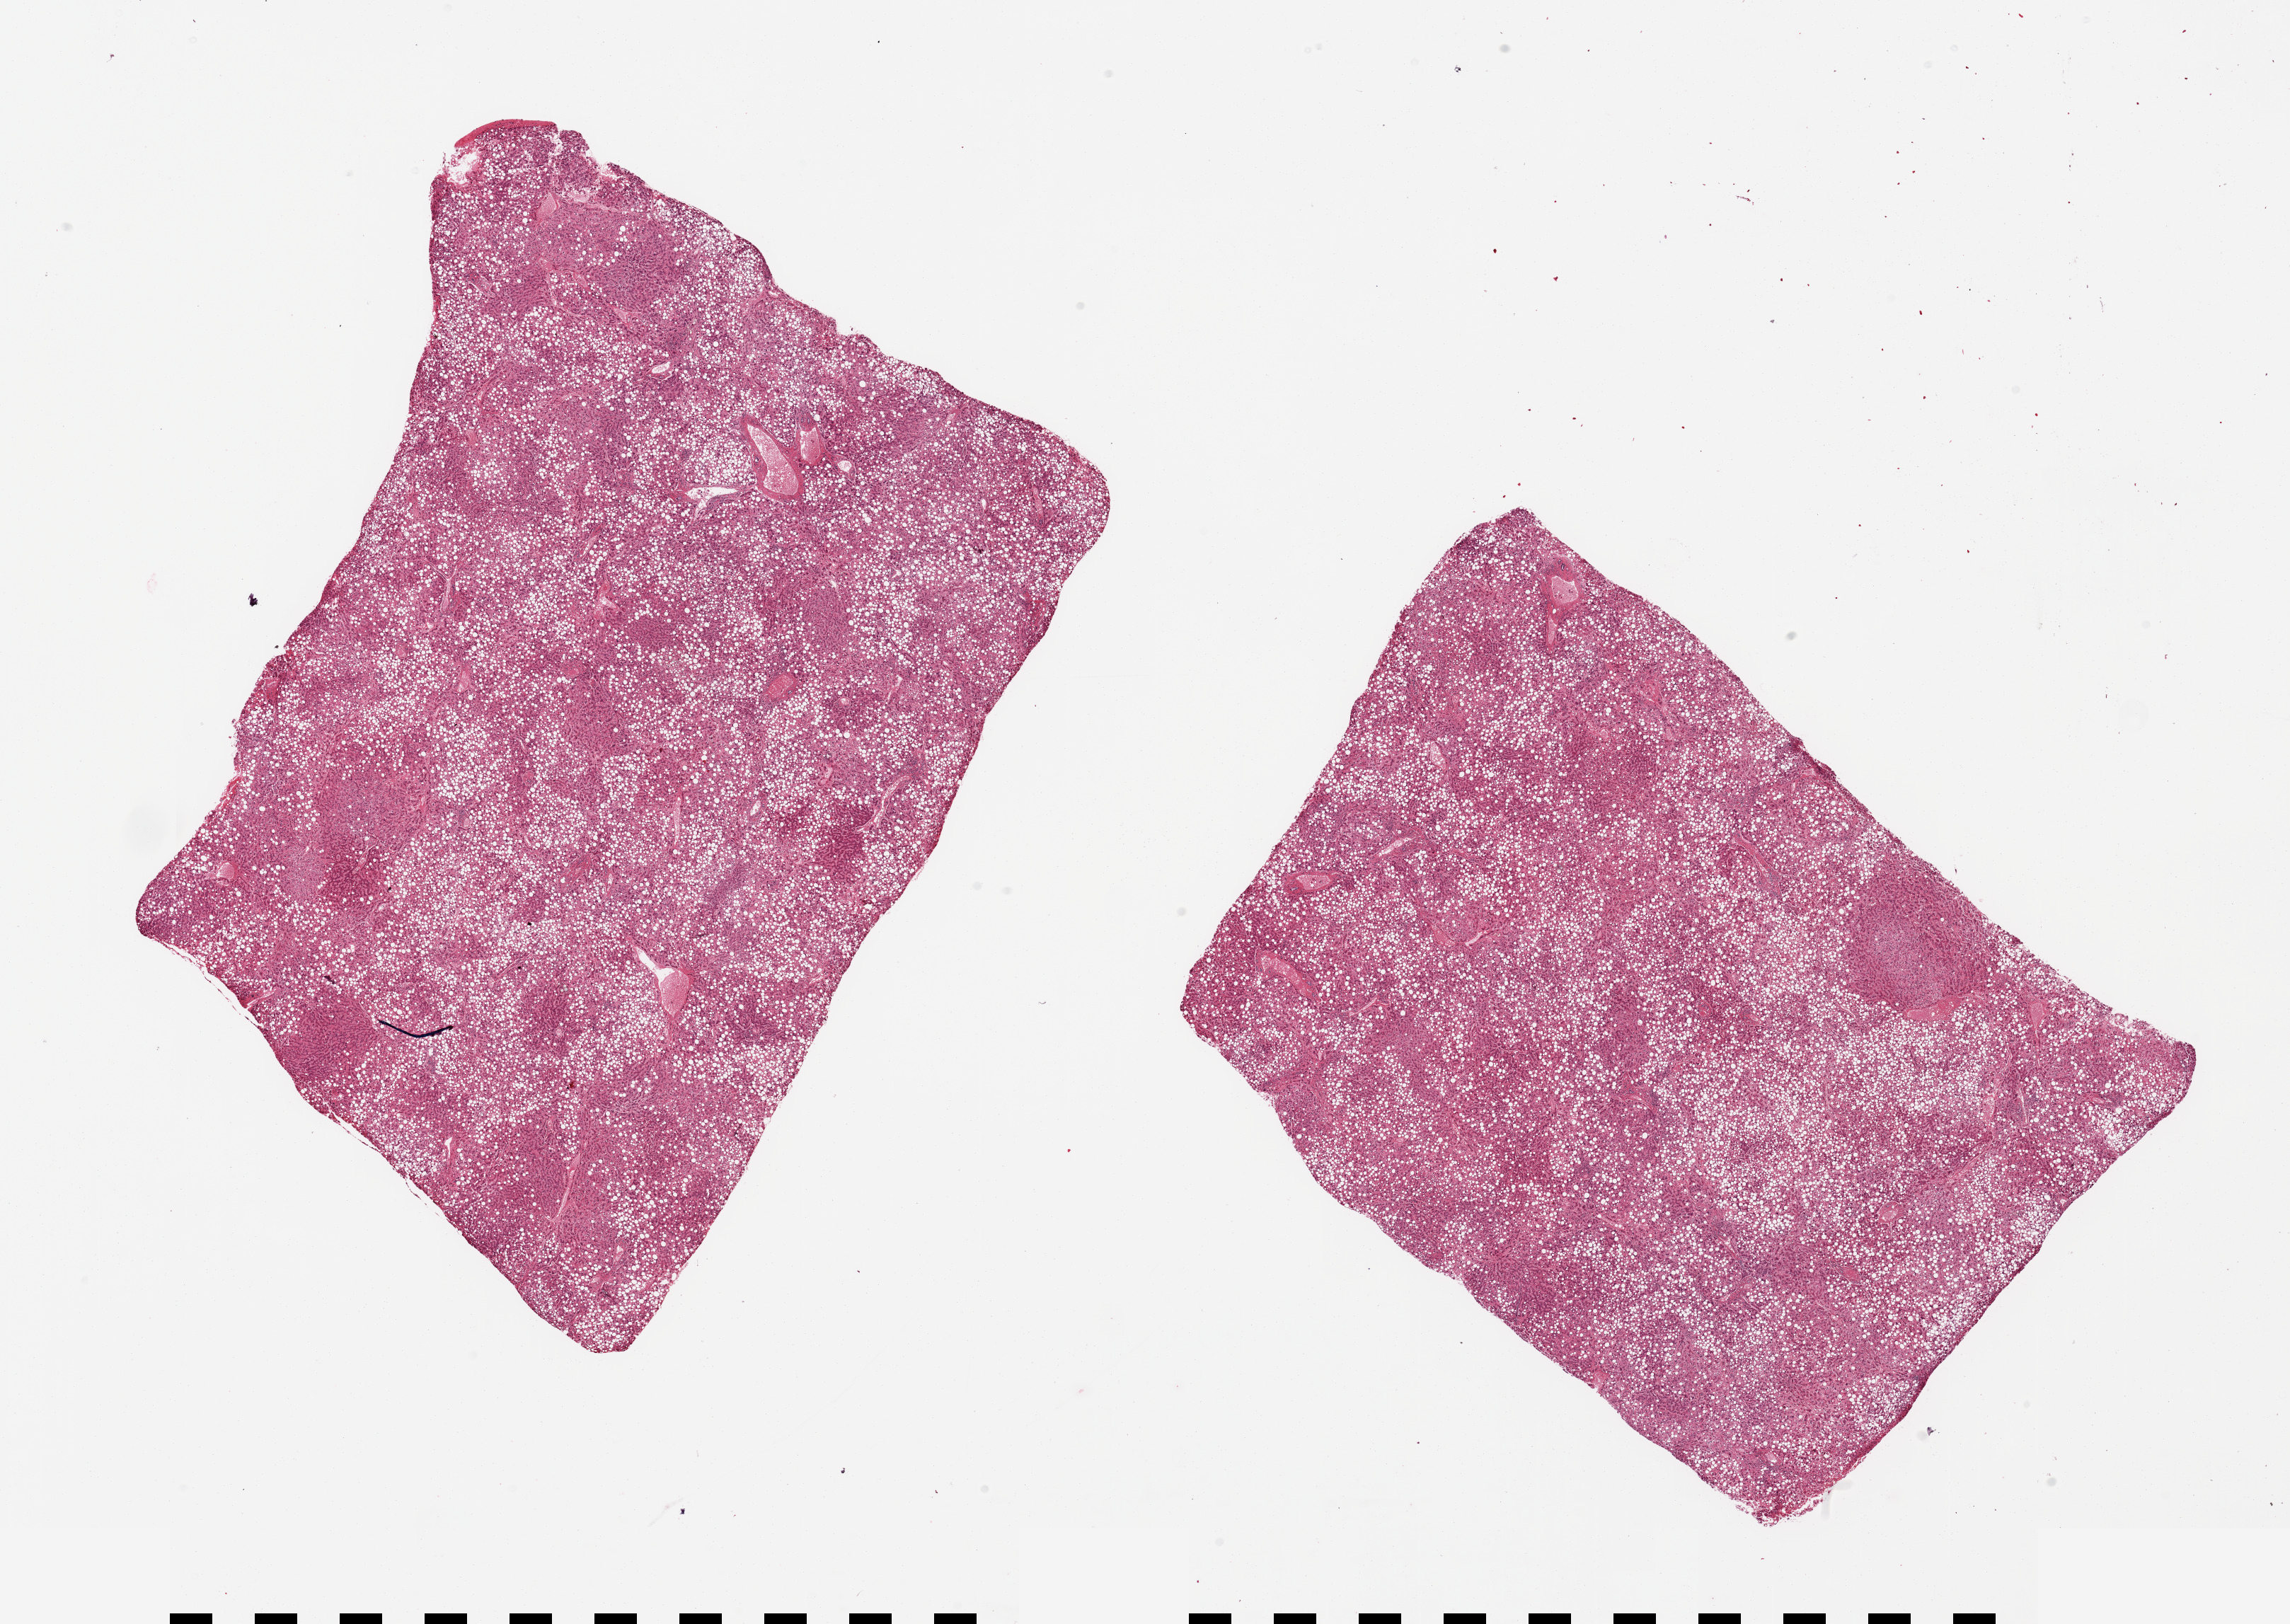
Whole-slide image, H&E stain, brightfield — whole scanned area (about 25.6 x 18.2 mm) shown as a low-resolution overview. PAXgene-fixed, paraffin-embedded tissue. Target tissue: liver. Donor tissue sample. Donor: male.
Reviewer comment on this tissue sample: 2 pieces; congestion and marked fatty change.